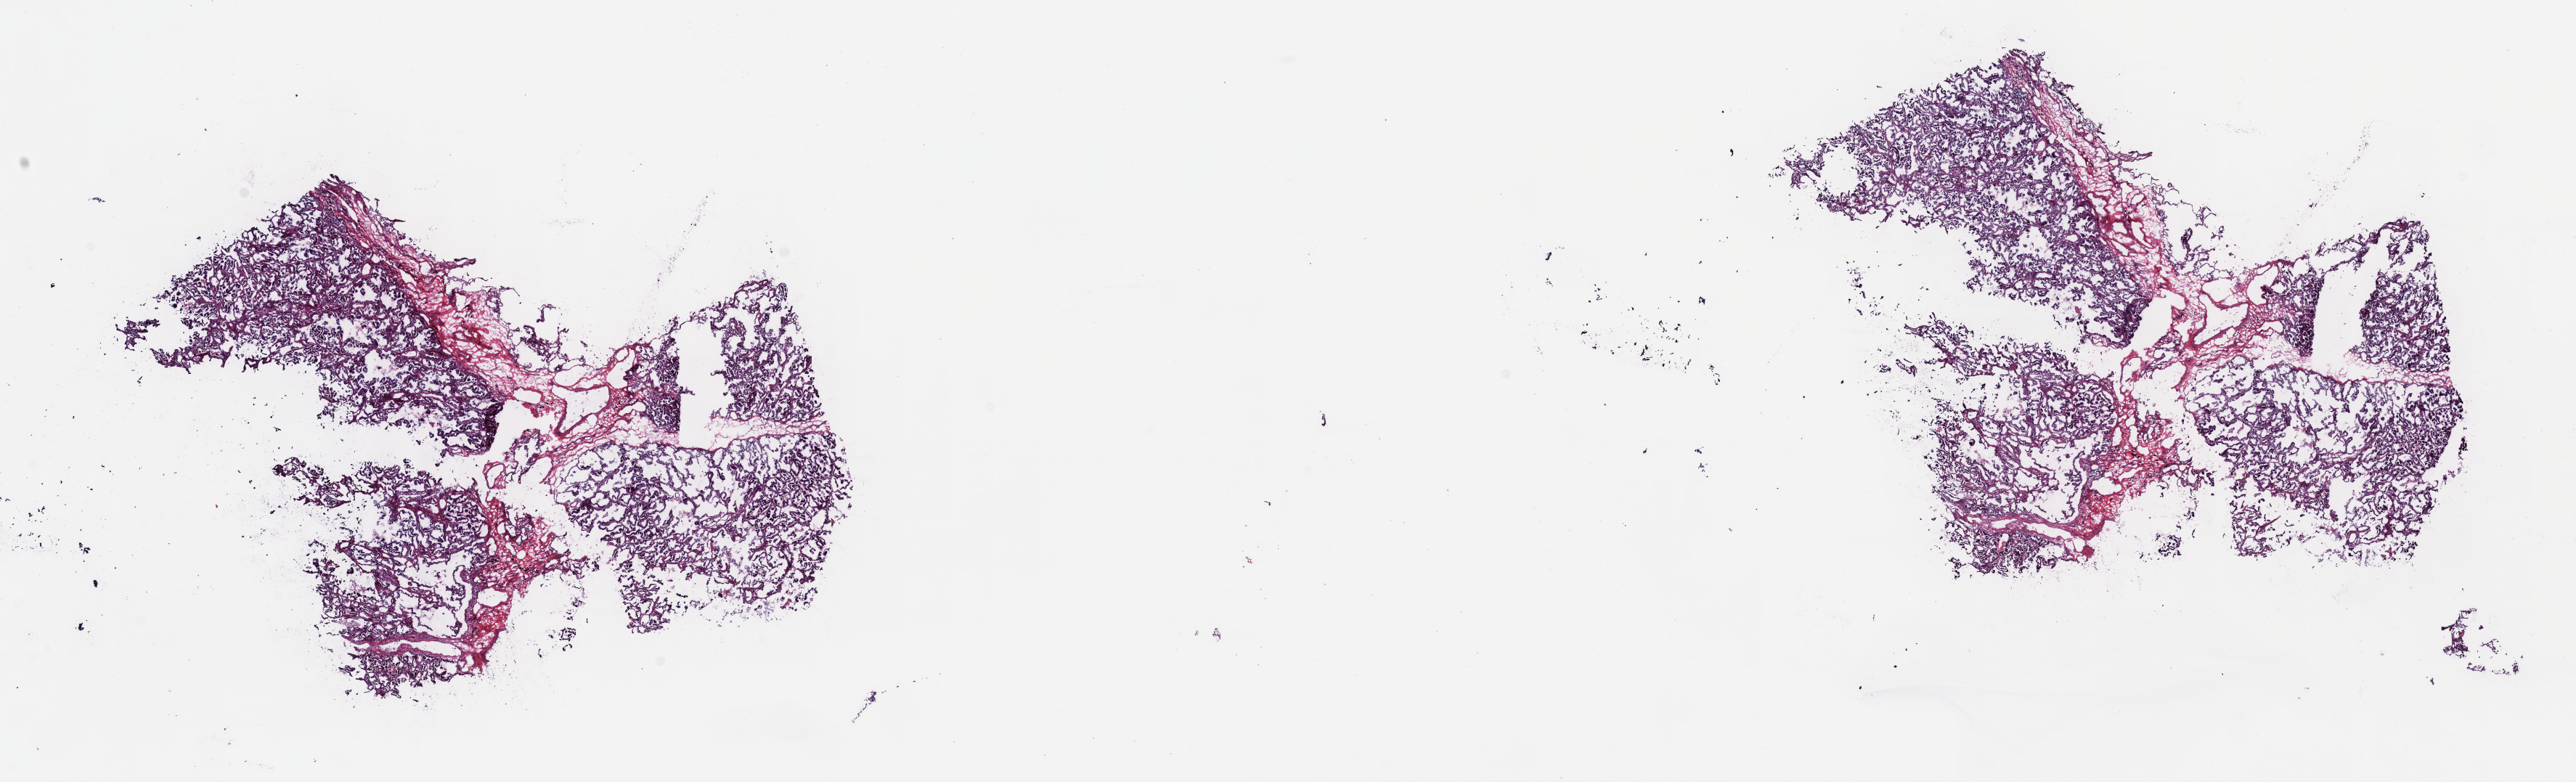
Whole-slide histology image, Hematoxylin and eosin (H&E) stained — whole scanned area (about 28.7 x 8.7 mm, acquisition: 40x scan) shown as a low-resolution overview. Frozen section from the top of the tissue portion. Lung, primary tumour sample. Male, age 49 years at initial diagnosis. Pathologist review of this section (percent, as recorded): tumour cells 73%, tumour nuclei 90%, normal cells 0%, stromal cells 25%, necrosis 2%. Inflammatory infiltration, as recorded: lymphocyte infiltration 6%, monocyte infiltration 1%, neutrophil infiltration 1%.
AJCC pathologic stage: IIIA. Histologic diagnosis: Adenocarcinoma, NOS (upper lobe, lung).